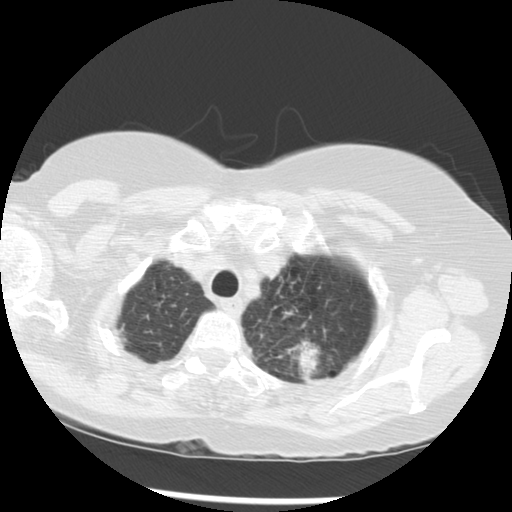
Axial slice from a low-dose chest CT screening exam. Third annual screen. Lung window (W 1500 / L -600 HU). Standard (soft-tissue) reconstruction kernel (STANDARD). 120 kVp. Slice 245 of 283 in the series. Female participant, aged 70 years at enrolment.
Expert-annotated lung lesion, bounding box <245,293,344,380> (left, top, right, bottom; pixels). The exam's reader record, not a measurement of the box and not confirmed to be the same lesion: non-calcified nodule or mass ≥4 mm, left upper lobe, 32 × 26 mm, spiculated (stellate) margins, soft tissue attenuation, pre-existing on the prior screen: yes; interval growth: yes. Later outcome: lung cancer diagnosed 24 days after this screen — neoplasm, malignant, left upper lobe, stage IIIB (AJCC 6th edition), 40 mm at pathology.